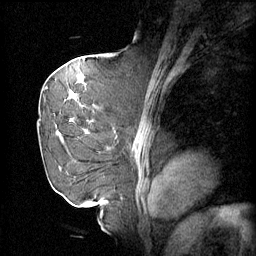
Breast MRI (dynamic contrast-enhanced), one sagittal slice. Position 35 of 60 along the scan axis. 4 images stored at this slice position (order not interpretable as contrast timing). 1.5 T. TE 4.2 ms, TR 11 ms. 256 × 256 image matrix, field of view 220 × 220 mm. Patient: female, 72 years.
Structures marked on this image (semi-automatic segmentation, software-assisted and operator-edited):
- analysis volume of interest (the breast-tissue region the enhancement analysis was run in; not a lesion): bounding box (x1, y1, x2, y2) in pixels: (44, 68, 109, 161)
- tumour enhancement mask (voxels above the 70 % enhancement threshold inside the analysis volume of interest): (53, 72, 103, 133)